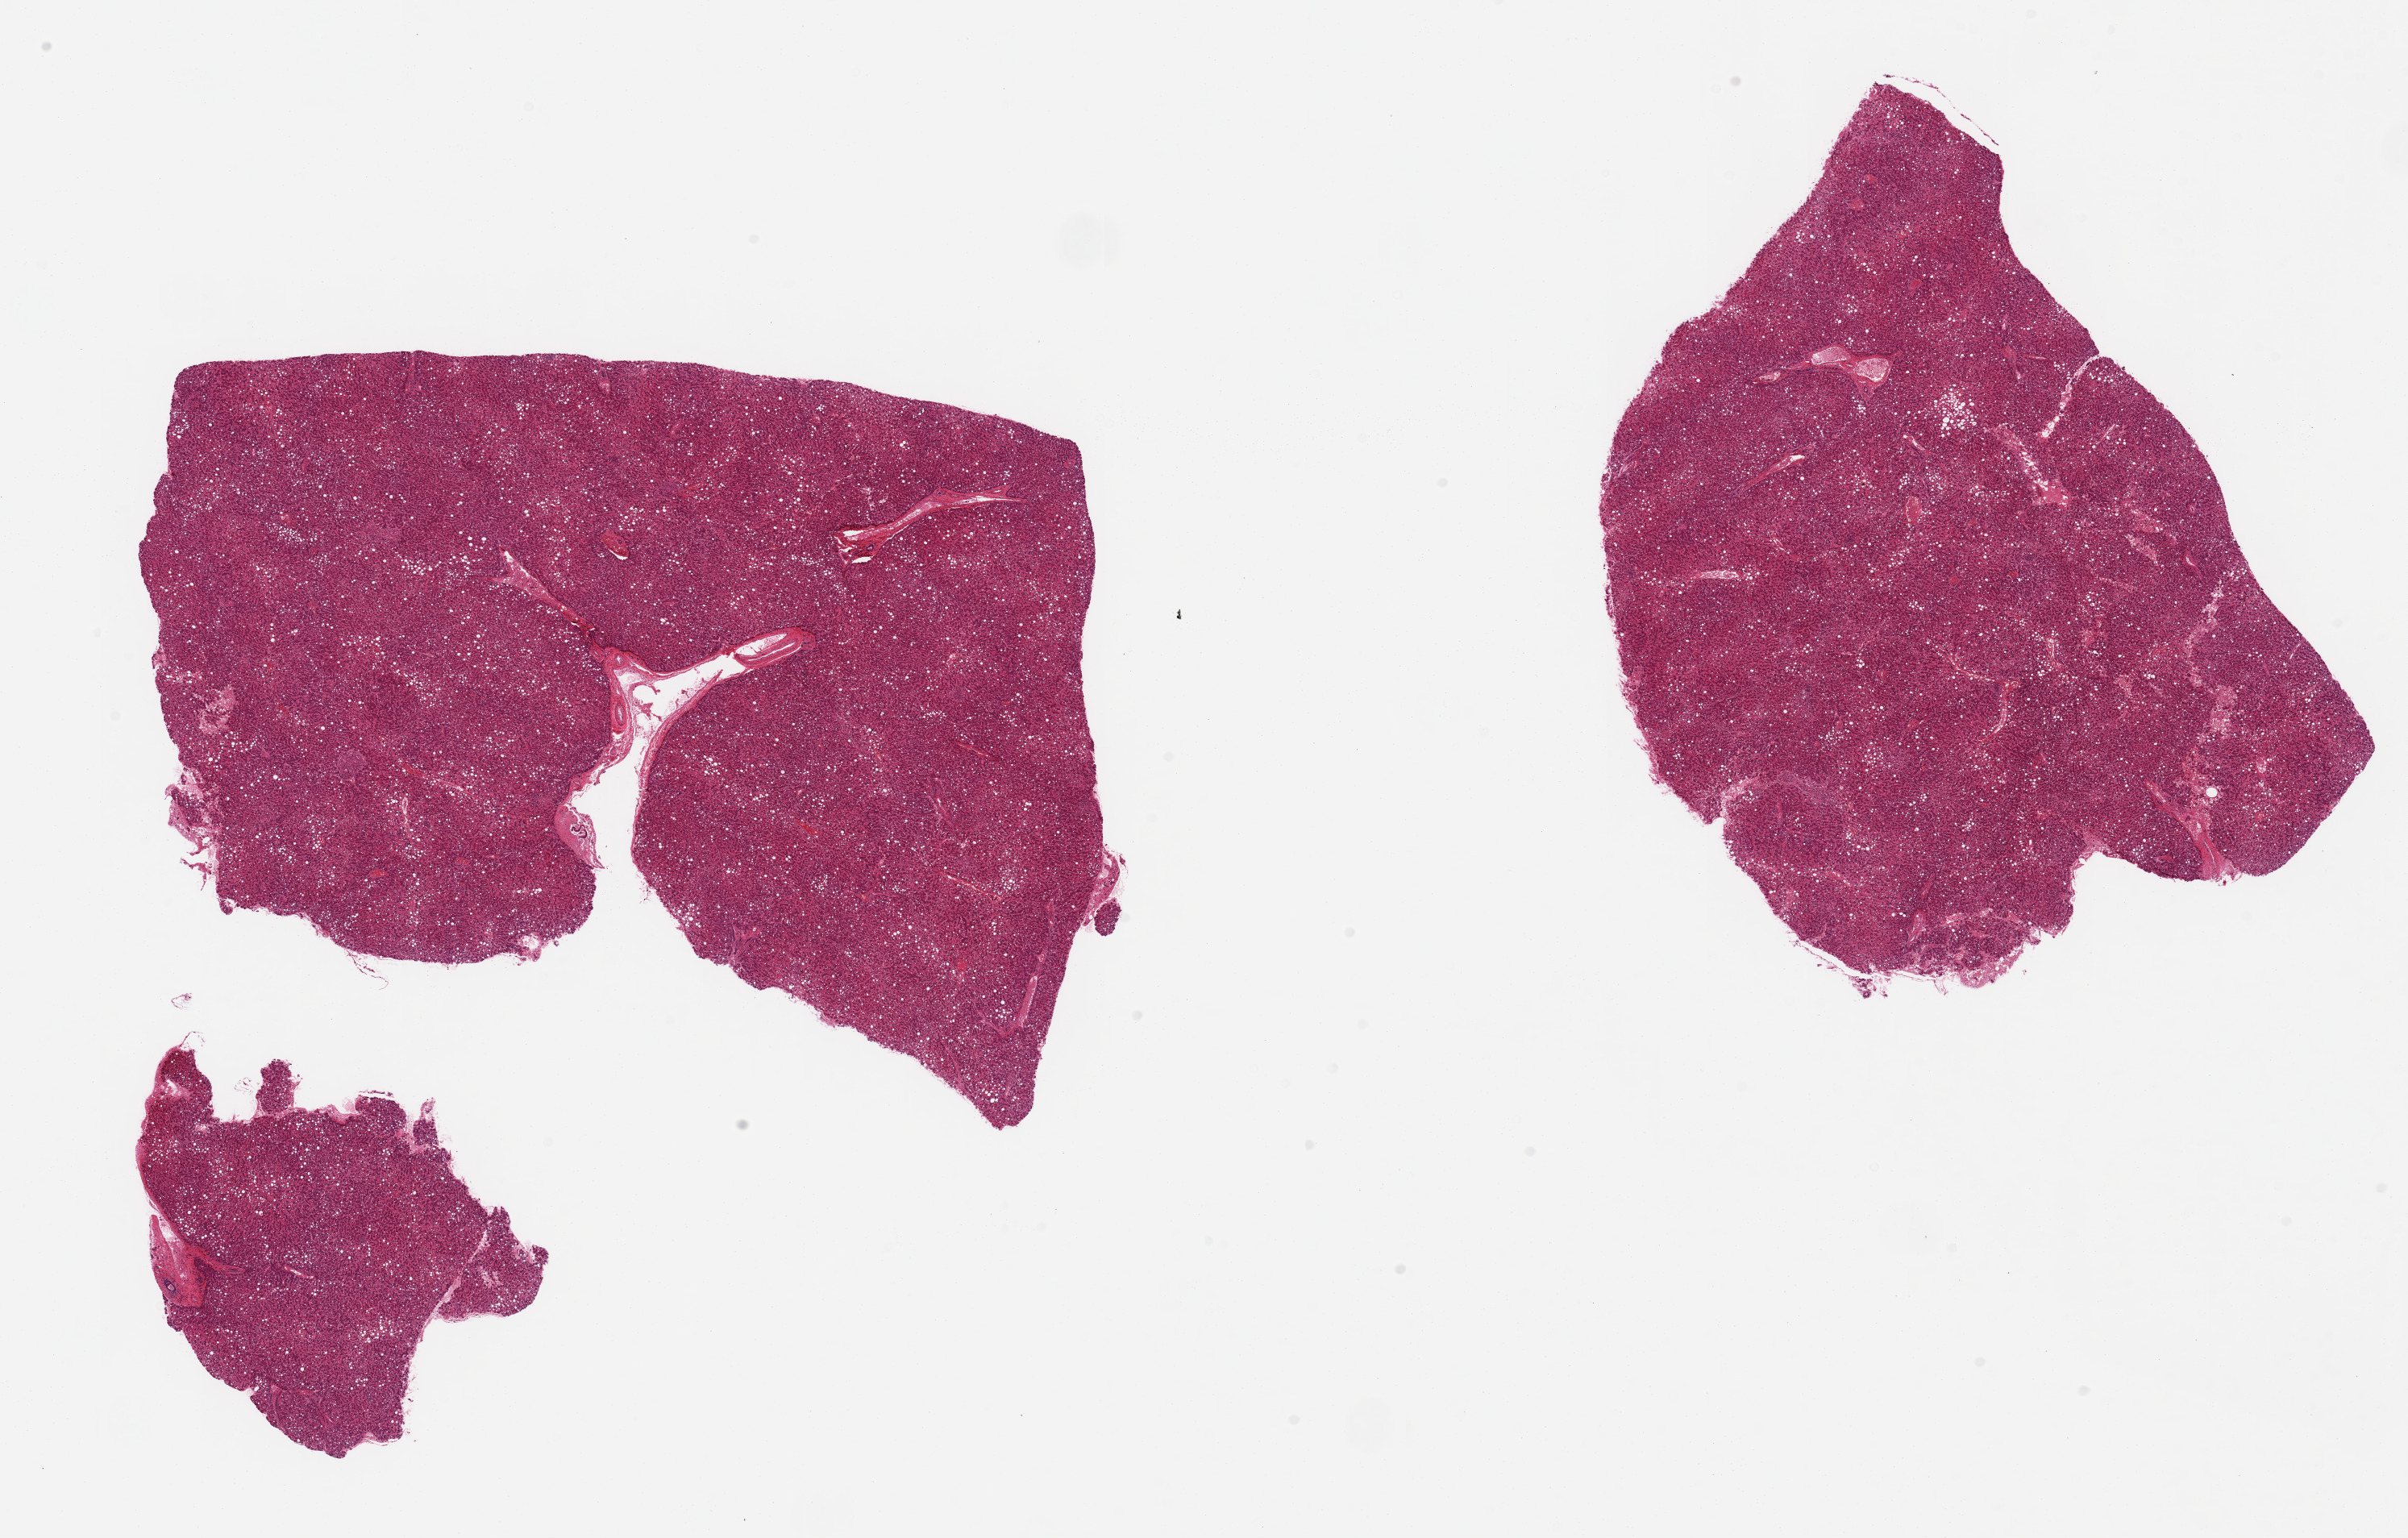
Whole-slide image, hematoxylin and eosin (H&E) stain, brightfield — low-resolution overview of the scanned area, about 23.6 x 15.1 mm (from a 20x scan), PAXgene-fixed paraffin-embedded (PFPE) section, section of liver (target tissue), donor tissue sample. Donor: male.
- pathologist's review note for this sample: 2 pieces, macrovesicular steatosis, moderate, ~30-40% of parenchyma